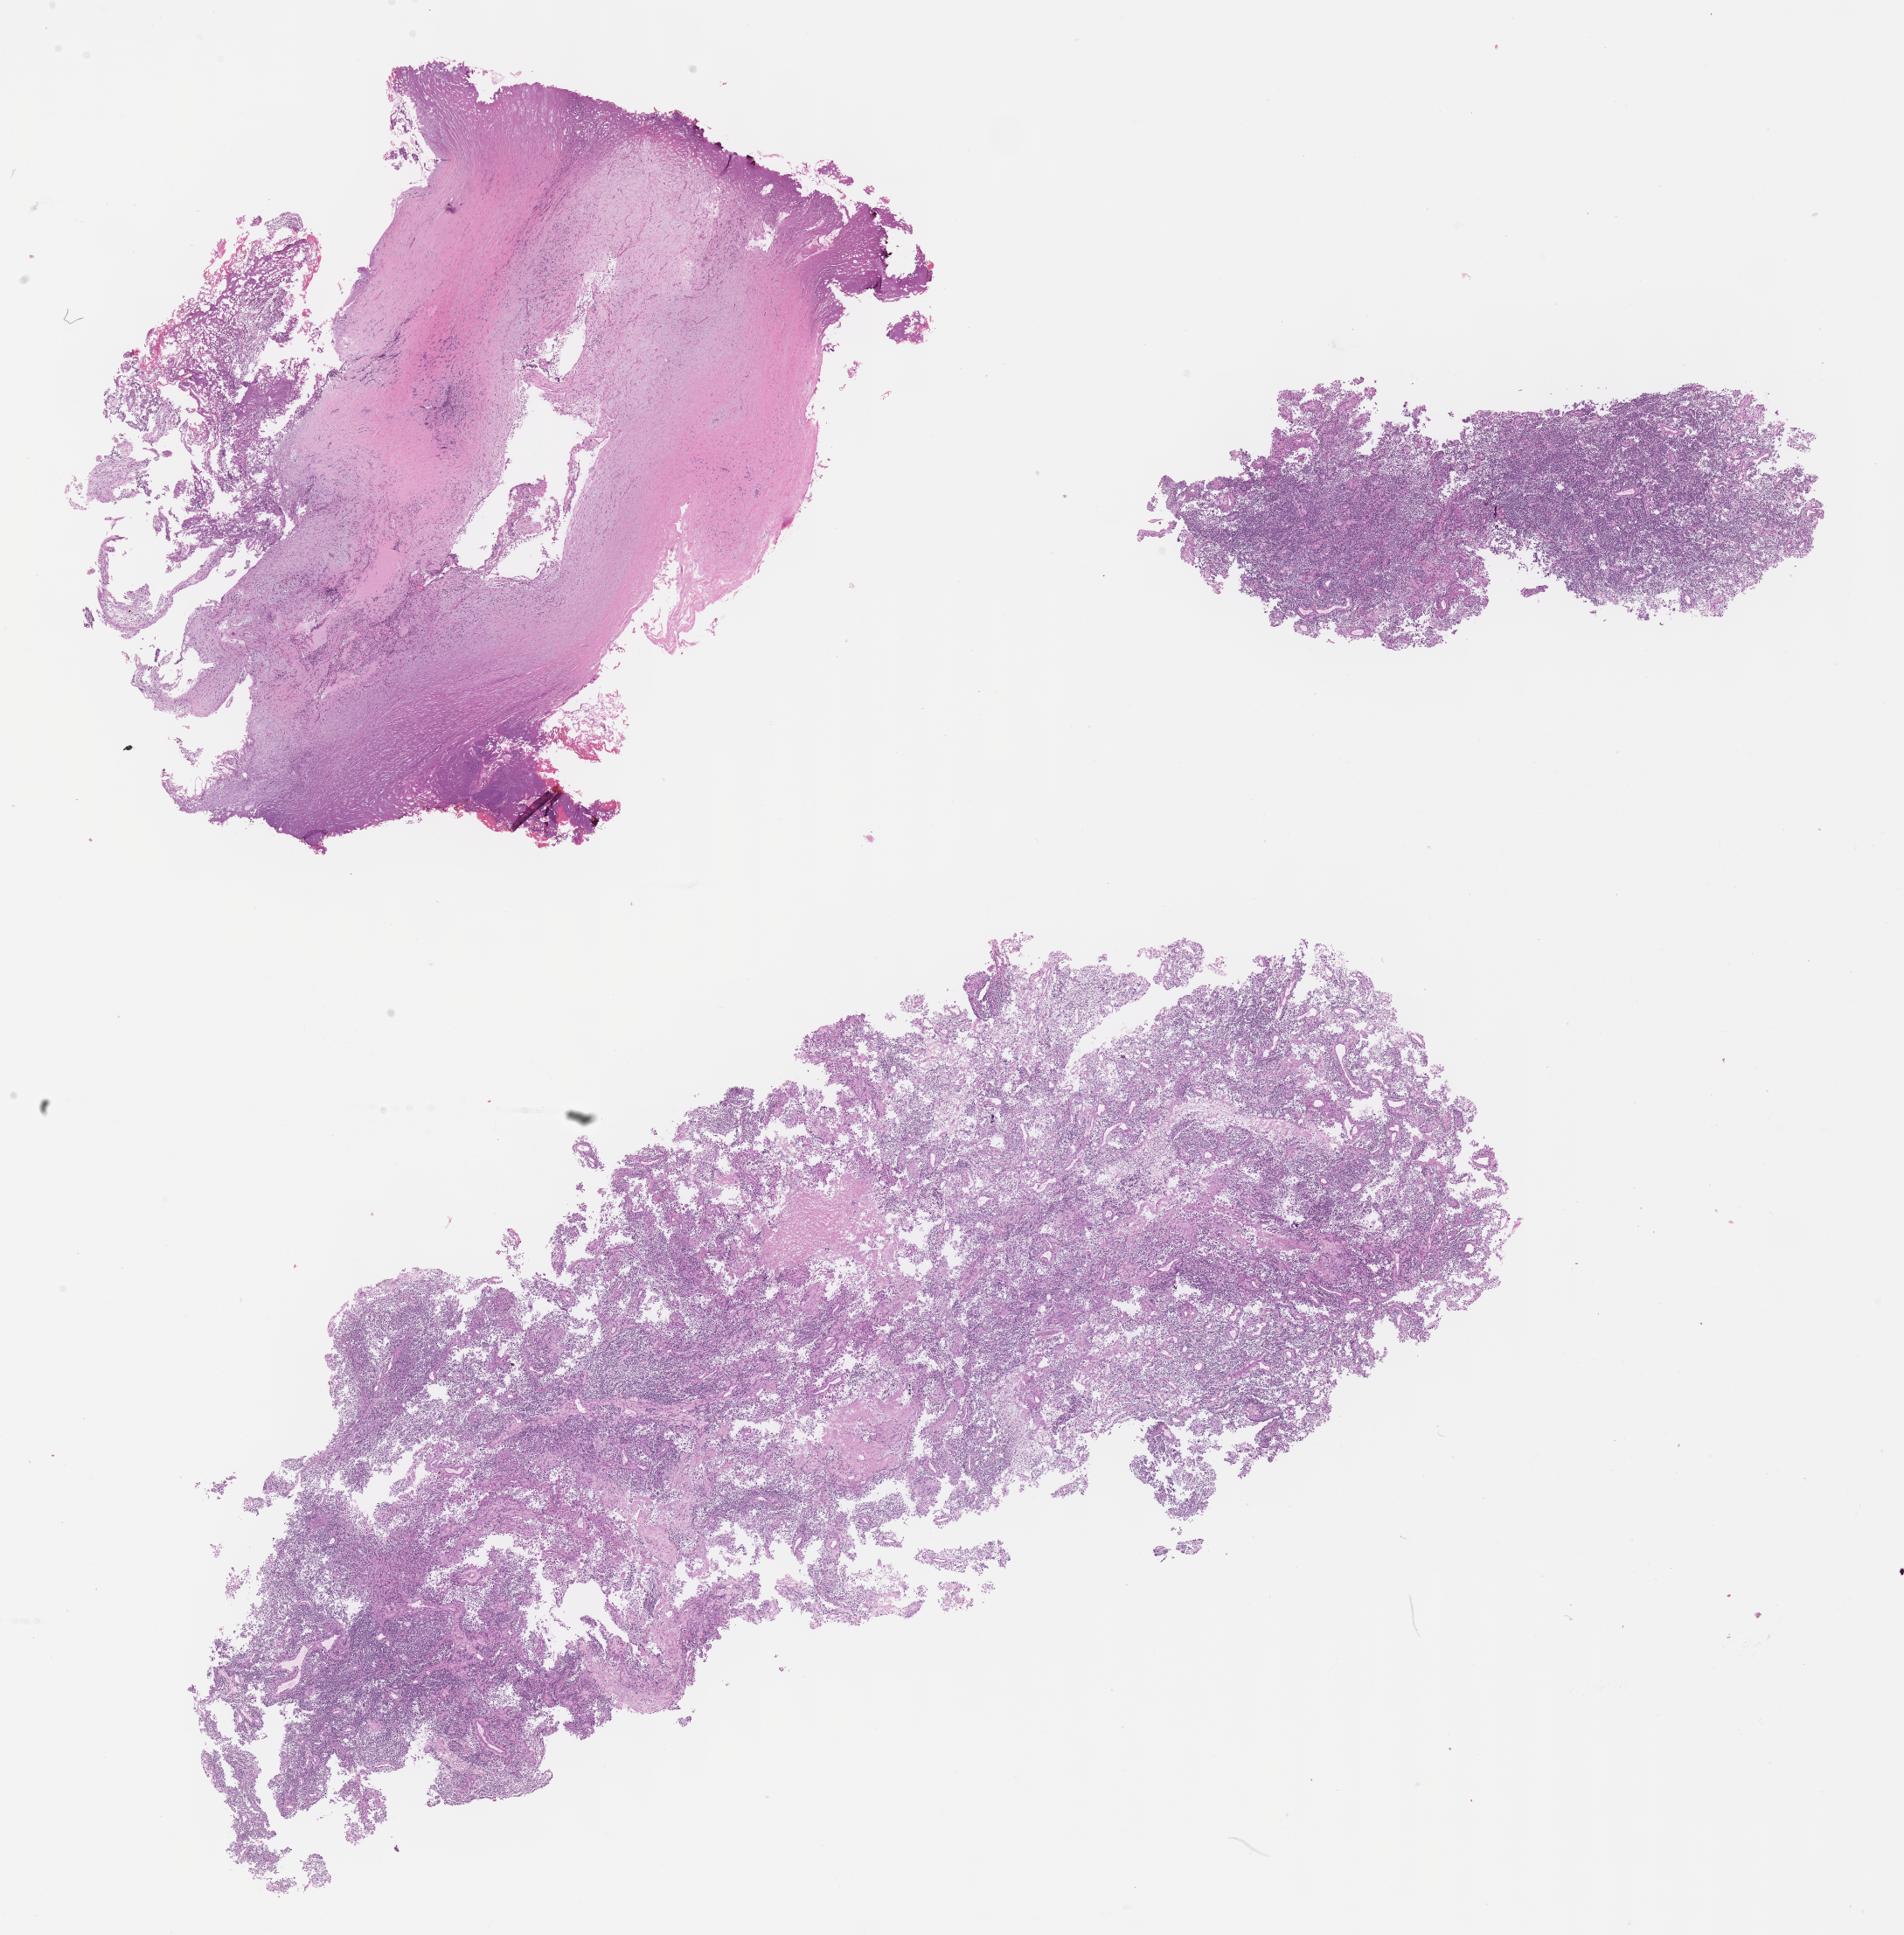
Digitized haematoxylin and eosin-stained section of tumor tissue, whole scanned area (about 17.6 x 17.9 mm) shown as a low-resolution overview; FFPE section; site: thigh. Male patient, age at diagnosis 6.2 years.
• metastatic status at presentation (as recorded): metastatic (confirmed)
• diagnosis: rhabdomyosarcoma; histological classification: alveolar rhabdomyosarcoma
• stage (as recorded): 4